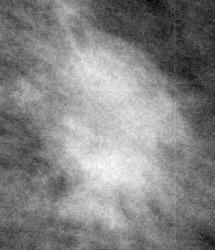
Cropped region of a digitized screen-film mammogram centred on a radiologist-marked abnormality, left breast, CC view.
Finding: mass, shape oval, margins microlobulated; BI-RADS assessment category 4; subtlety rating 5 on a 1 (subtle) to 5 (obvious) scale; pathology result (as recorded, not read from the image): malignant.